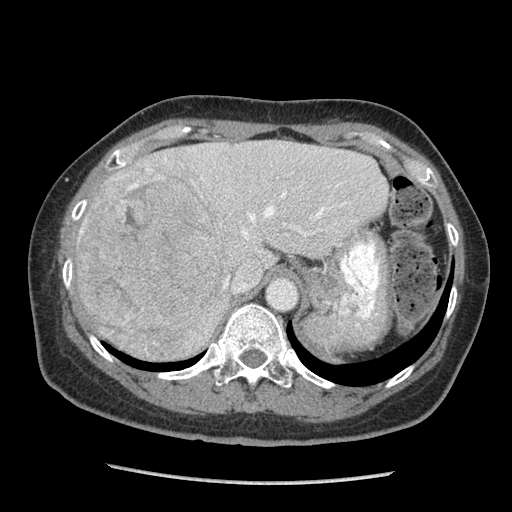
Contrast-enhanced abdominal CT (liver protocol), one axial slice. Position 65 of 105 along the scan axis. Soft-tissue window (W 400 / L 40 HU). 2.5 mm slice thickness. 512 × 512 image matrix, field of view 340 × 340 mm. From the clinical record (not read from this slice): diagnosis: hepatocellular carcinoma (patient treated with transarterial chemoembolisation; whether this scan precedes or follows treatment is not stated here); TNM stage (as recorded): Stage-I.
Annotated regions visible in this slice (semi-automatic segmentation, software-assisted and operator-edited):
- abdominal aorta: bounding box (x1, y1, x2, y2) in pixels: (268, 278, 297, 309)
- liver parenchyma outside the tumour (the mass and vessels are separate outlines, so this box may not span the whole liver): (76, 140, 388, 360)
- mass: (76, 163, 225, 350)
- liver vessels: (80, 157, 346, 289)